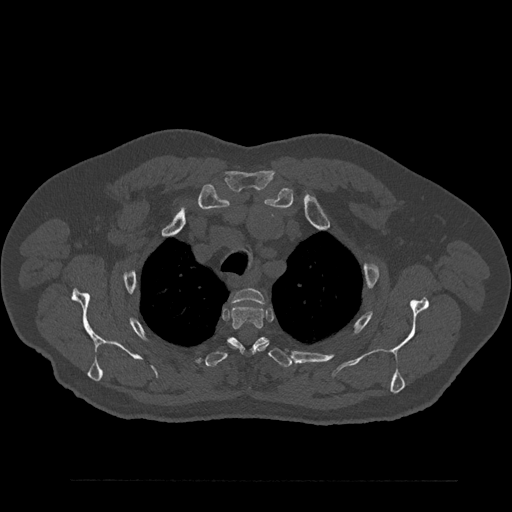
CT including the spine, one axial slice. Slice 674 of 797 in the series (ordered by position). Reconstruction kernel Br40s/3. Bone window (W 1800 / L 400 HU). 512 × 512 image matrix, field of view 430 × 430 mm. Patient: male, 61 years. From the clinical record (not read from this slice): primary cancer: prostate.
Outlined on this slice (semi-automatic segmentation, software-assisted and operator-edited):
- T2 vertebra: bounding box (x1, y1, x2, y2) in pixels: (232, 288, 265, 304)
- T3 vertebra: (231, 305, 267, 352)
- T4 vertebra: (205, 337, 292, 368)